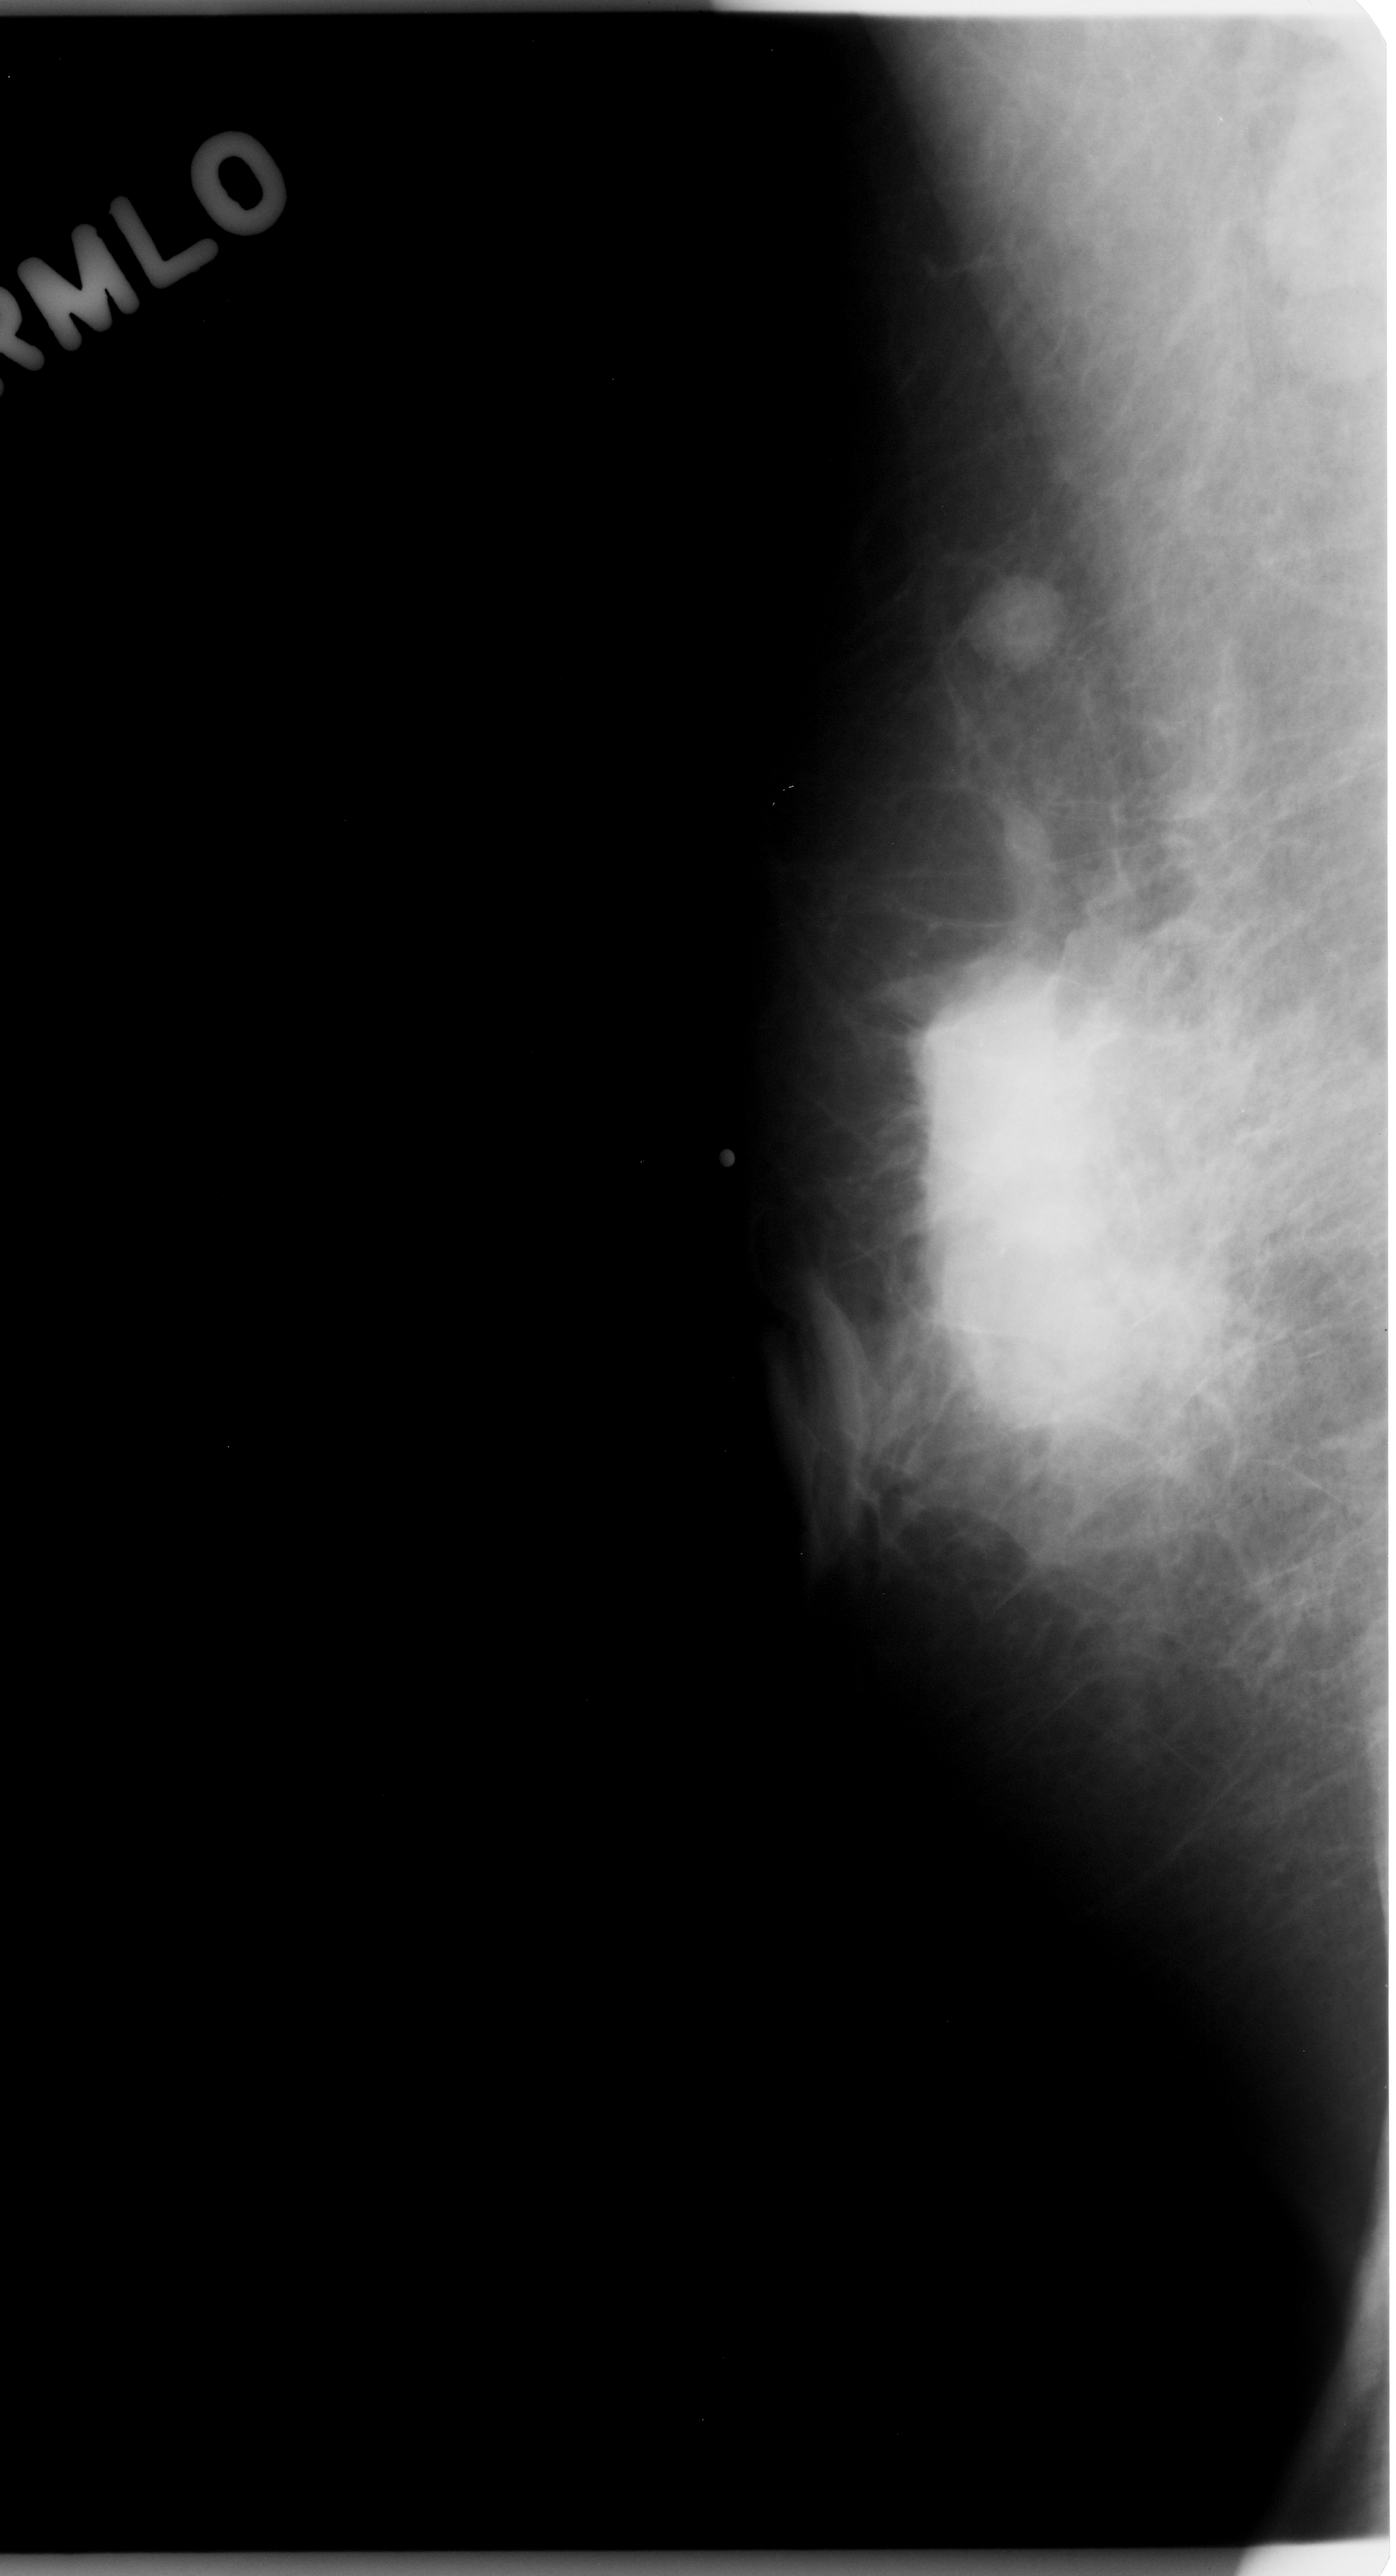
Mammogram (digitized film); right breast; MLO view; breast composition: heterogeneously dense (BI-RADS density category 3 of 4).
Marked findings (only marked abnormalities are described; nothing is implied about the rest of the image): mass, shape round, margins circumscribed; BI-RADS assessment category 5; pathology result (as recorded, not read from the image): malignant.